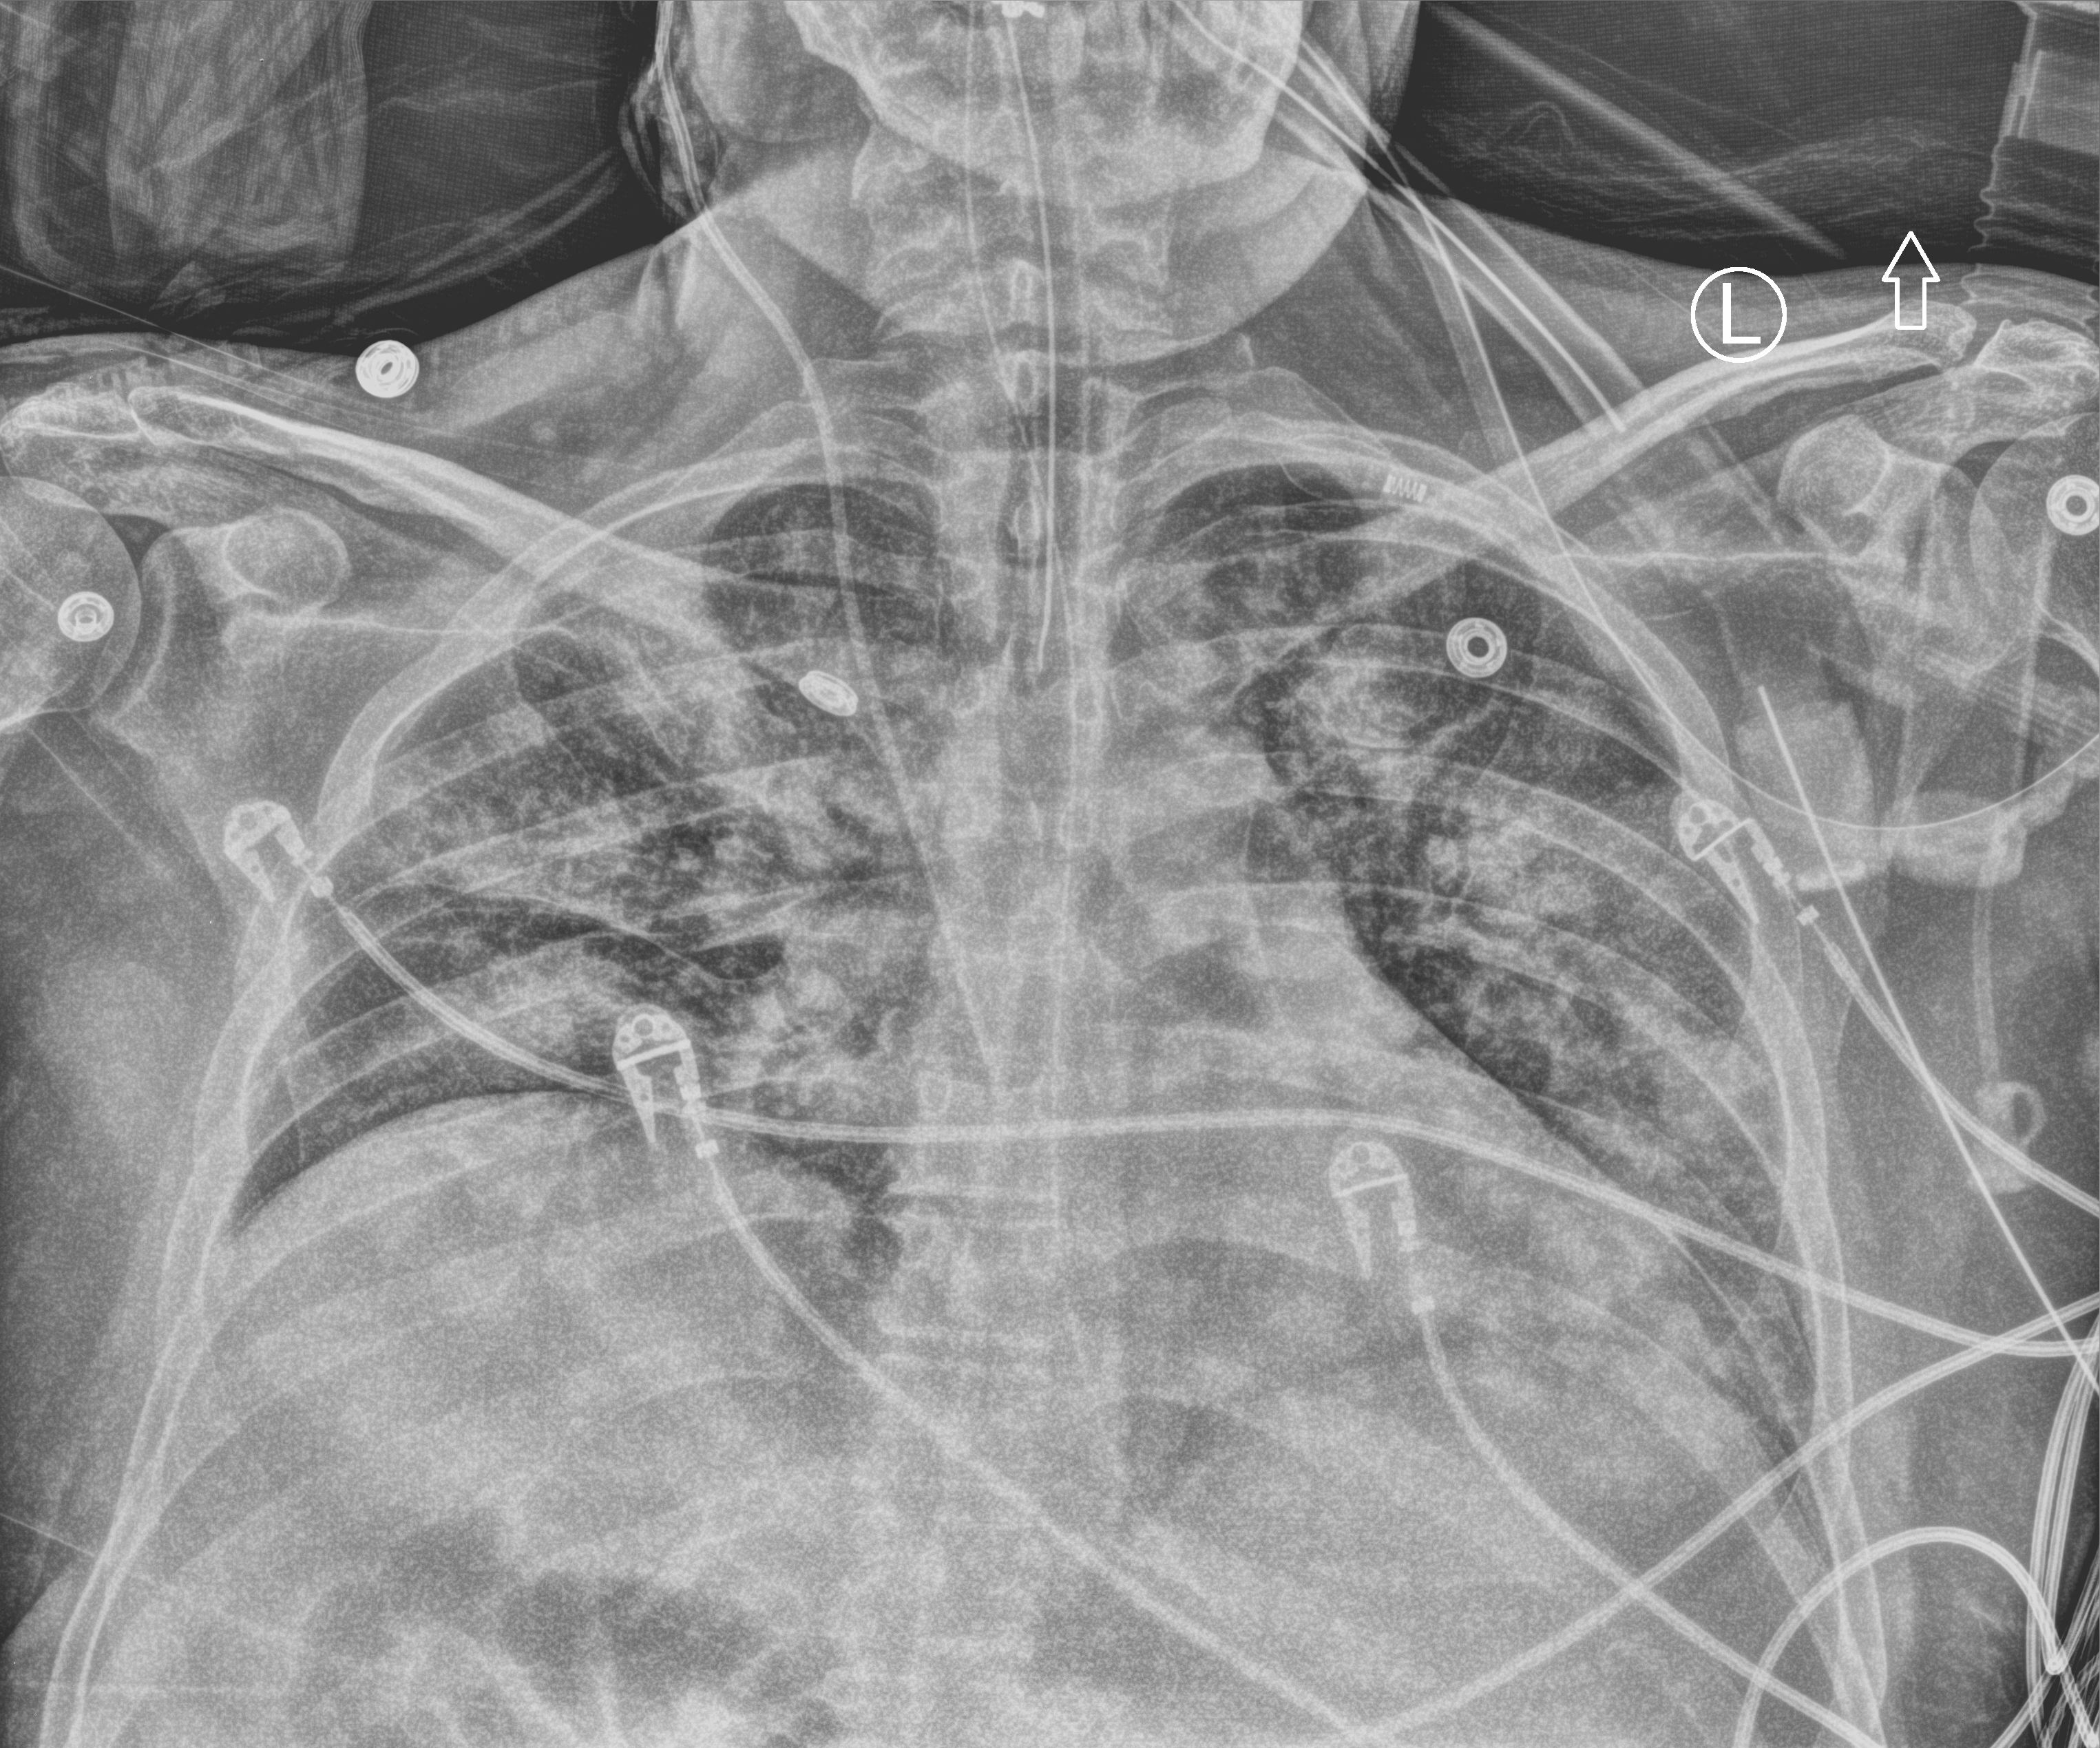
Chest X-ray (portable); anteroposterior (AP) projection. Patient hospitalised with COVID-19; male, aged 18–59 years.
Admission-level facts for this patient (not findings on this image; timing relative to this image not recorded): chronic kidney disease (admission record): no; hypertension (admission record): no.